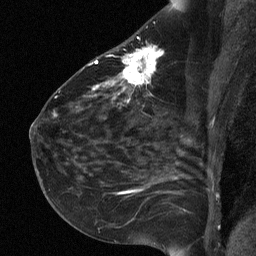
Breast MRI (dynamic contrast-enhanced), one sagittal slice; position 37 of 64 along the scan axis; dynamic contrast-enhanced study with each time point stored as its own series, time point 2 of 3 at this slice position (early post-contrast, ordered by acquisition time); 1.5 T; TE 4.8 ms, TR 27 ms; 2 mm slice thickness; 256 × 256 image matrix. Female patient, age 51 years. Case-level facts recorded for this patient, not image findings: setting: breast cancer imaged before/during neoadjuvant chemotherapy; receptor status: HR-positive, HER2-negative.
Annotated regions visible in this slice (semi-automatically segmented with operator editing):
- analysis volume of interest (the breast-tissue region the enhancement analysis was run in; not a lesion): box from (x=72, y=34) to (x=180, y=118) px
- tumour enhancement mask (voxels above the 90 % enhancement threshold inside the analysis volume of interest): (x=92, y=46)–(x=161, y=103)